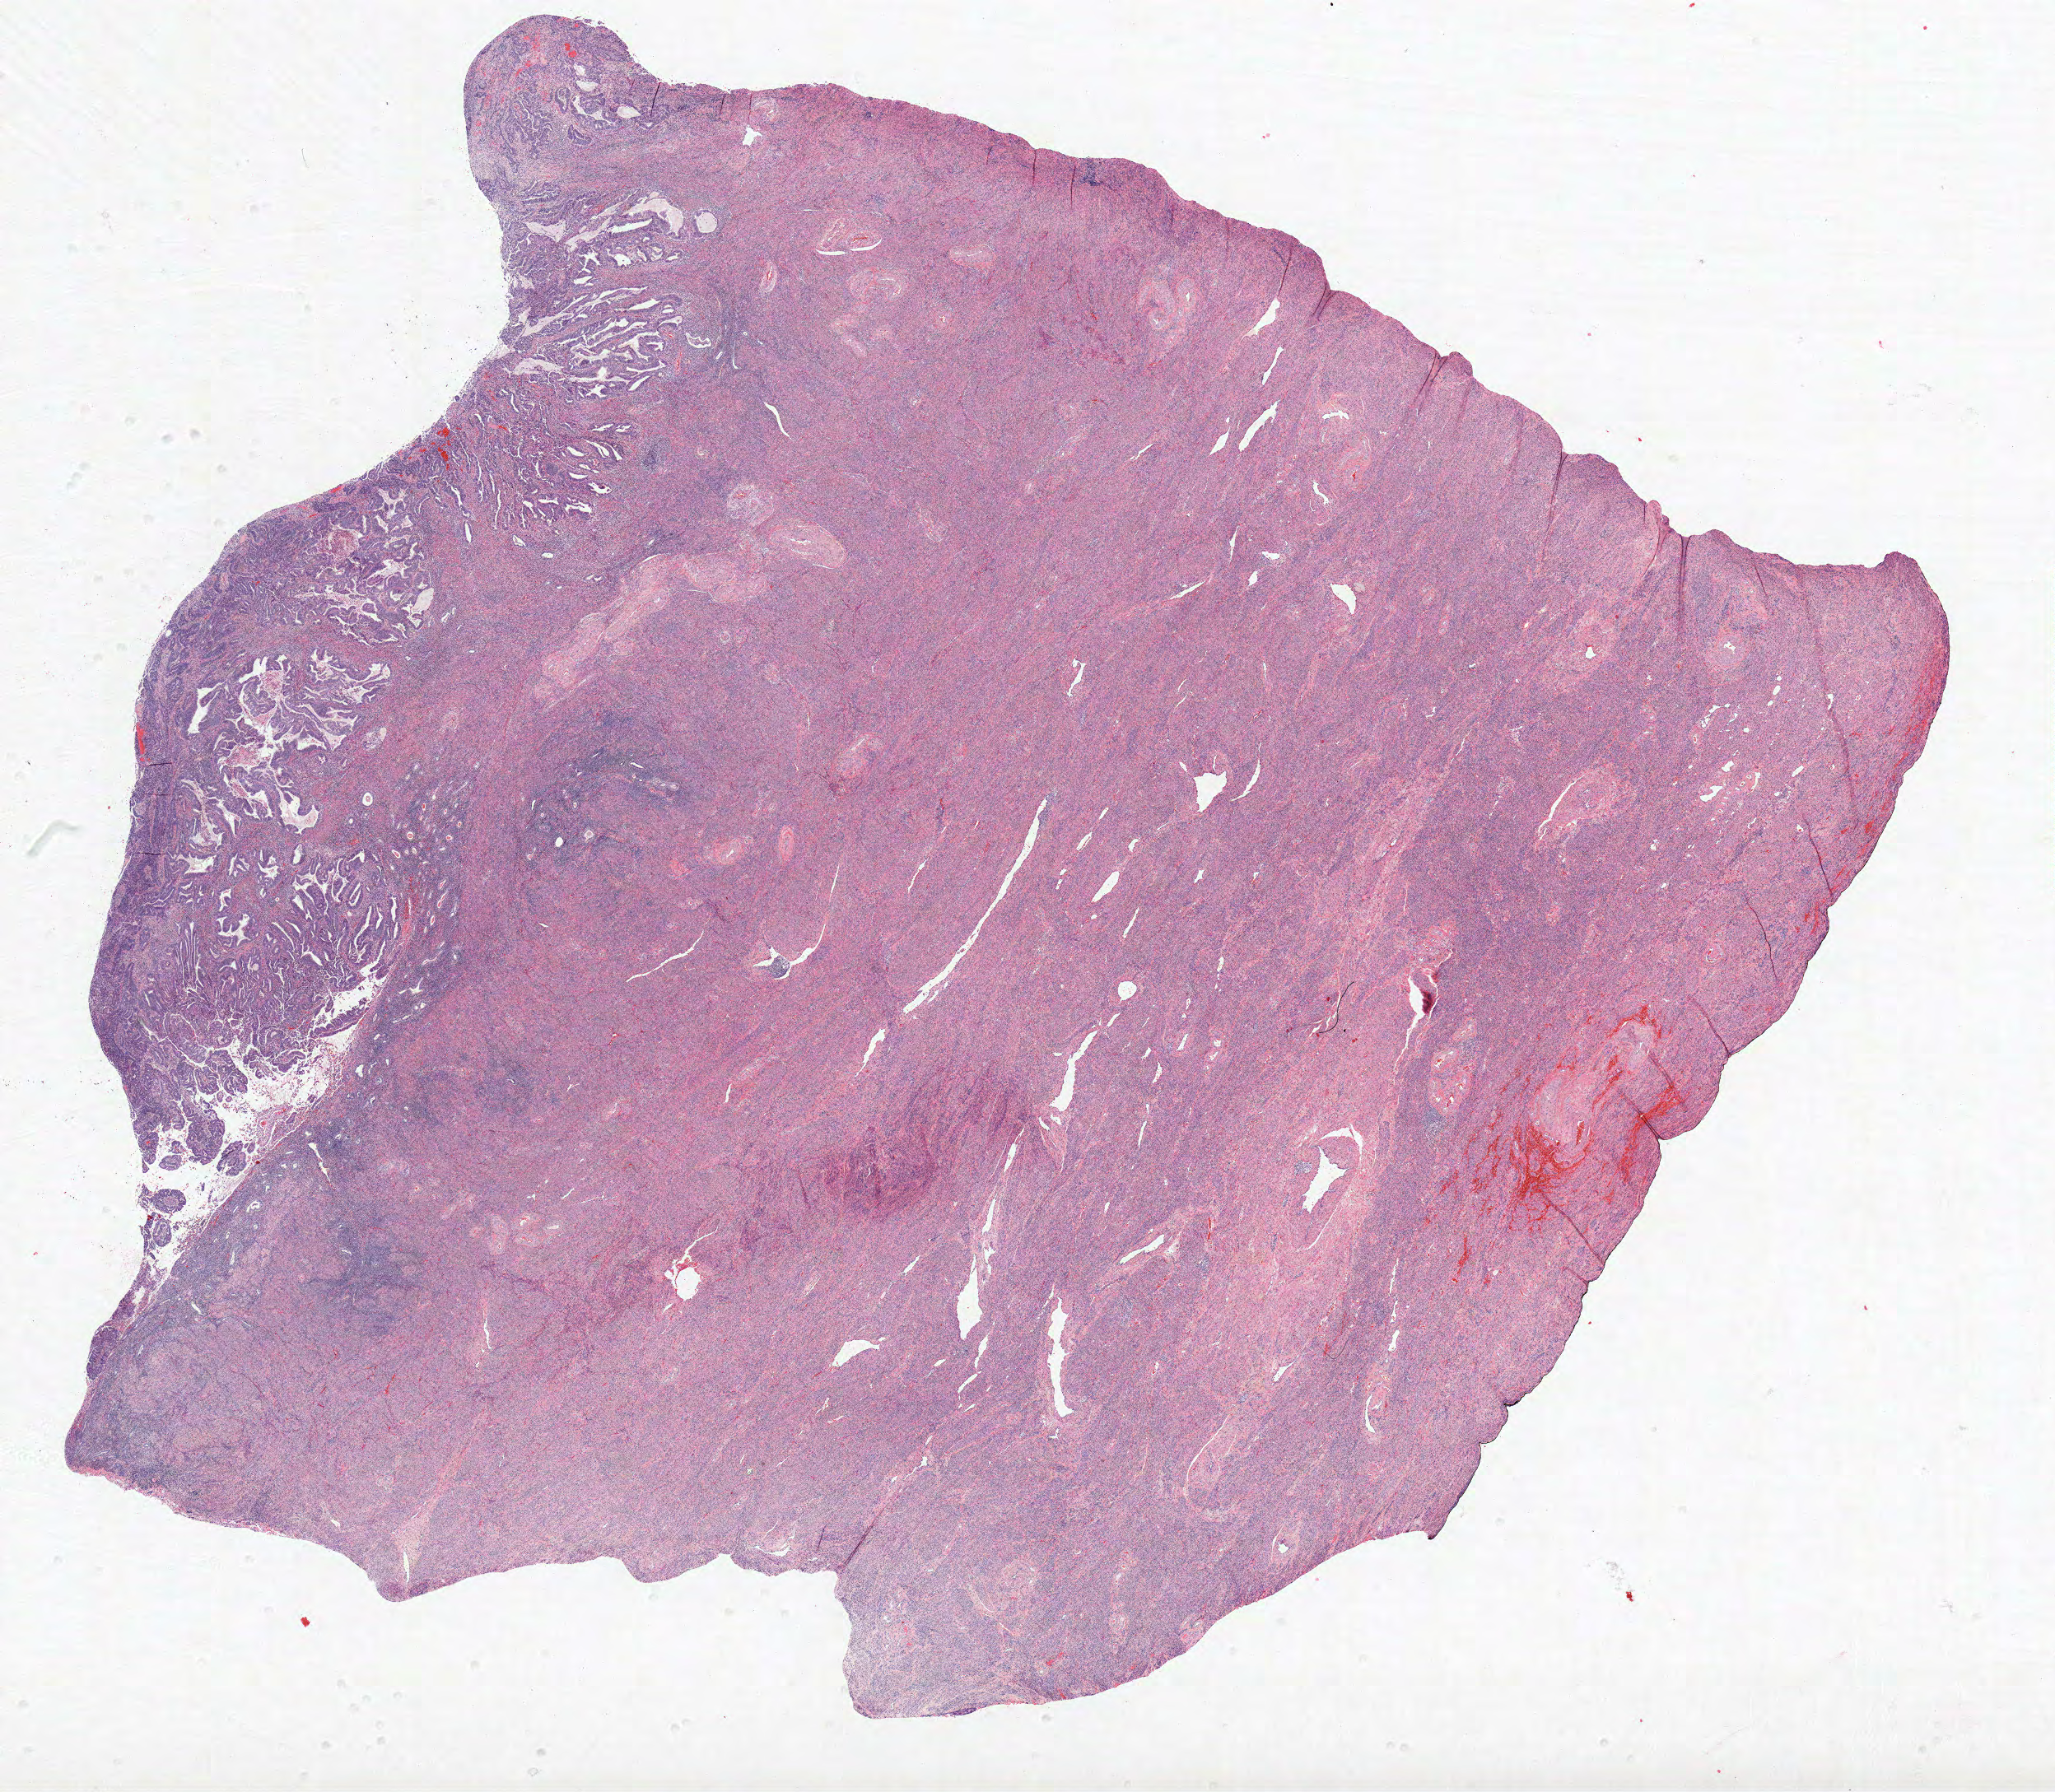
Digitized Hematoxylin and eosin (H&E) stained tissue section (whole slide) — a low-resolution overview of the entire scanned area, about 19.9 x 17.3 mm; formalin-fixed paraffin-embedded (FFPE) diagnostic section; uterus, primary tumour sample. Patient: female, age at initial diagnosis 60 years. Histologic grade: G1 (well differentiated).
* FIGO stage: IA
* pathologic diagnosis: Endometrioid adenocarcinoma, NOS